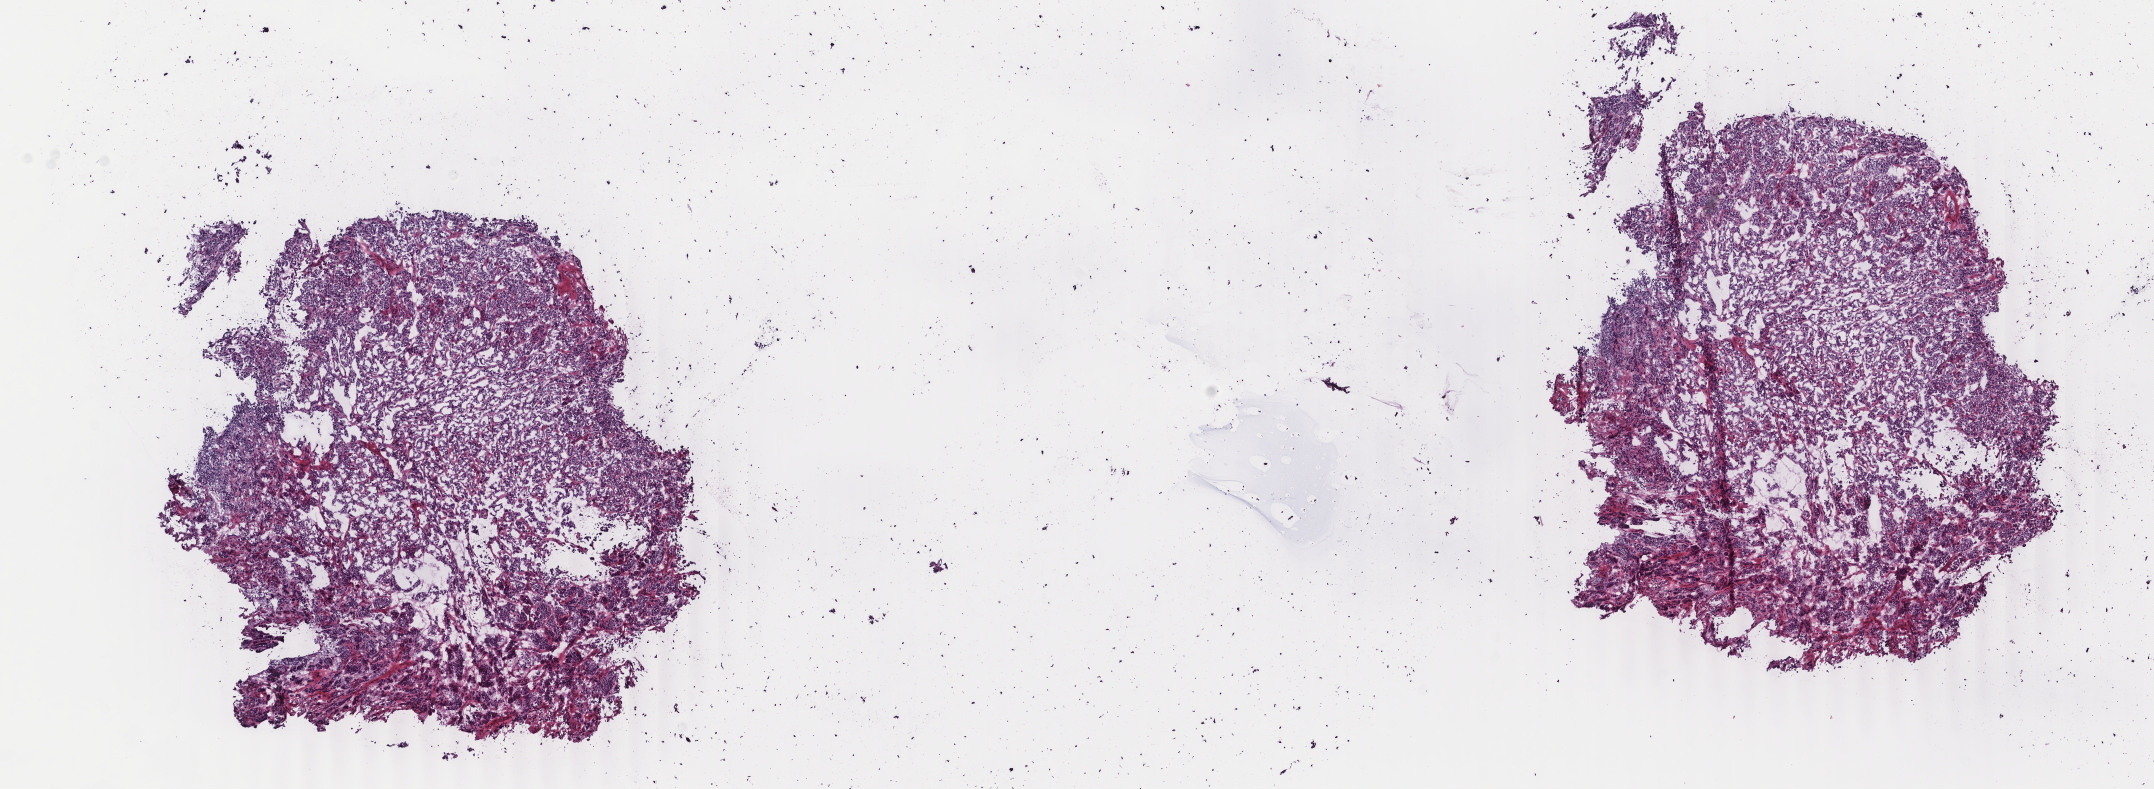
H&E whole-slide image, shown as a low-resolution overview of the whole scanned area (about 17.1 x 6.3 mm); frozen section; sample: primary tumour, thyroid. Male patient; age at initial diagnosis 36 years. Slide review estimates, as recorded: tumour cells 100%, tumour nuclei 85%, normal cells 0%, stromal cells 0%, necrosis 0%. Inflammatory infiltration, as recorded: lymphocyte infiltration 0%, monocyte infiltration 0%, neutrophil infiltration 0%.
Pathologic diagnosis: Papillary carcinoma, follicular variant (thyroid gland). AJCC pathologic stage: I (7th edition). Lymph nodes positive (case pathology): 0 of 9 examined.